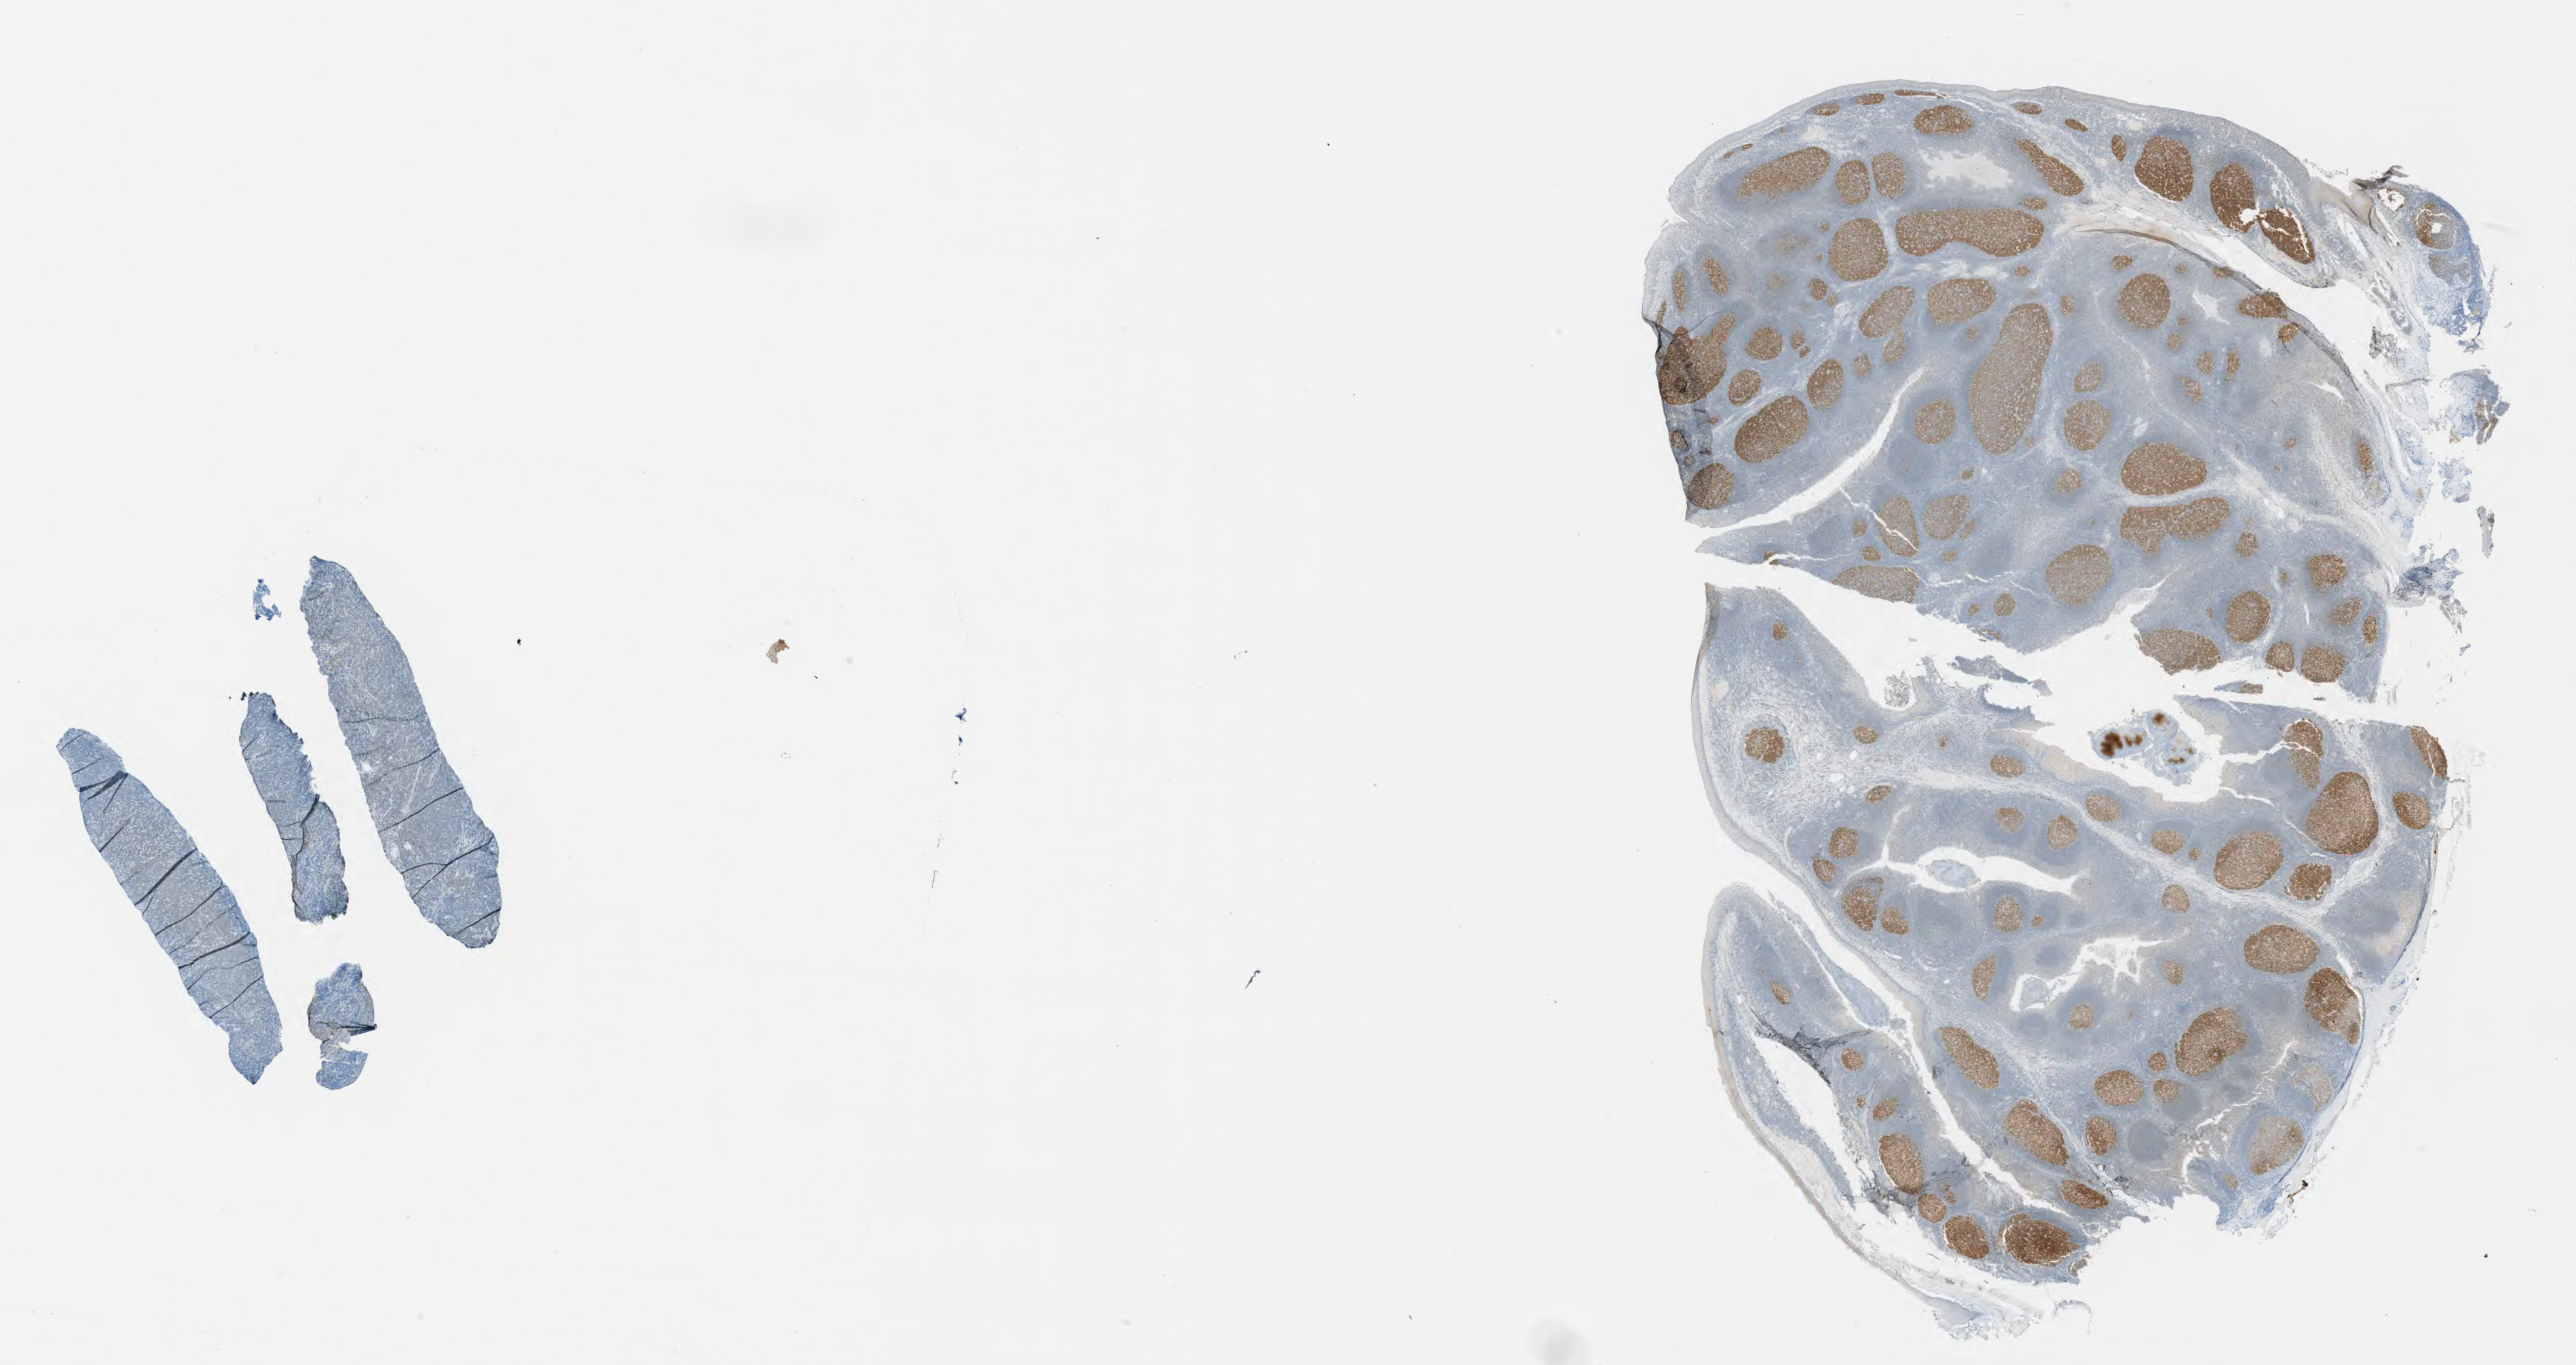
Immunohistochemistry (IHC) whole-slide image stained for BCL6, shown as a low-resolution overview of the whole scanned area (about 29.2 x 15.5 mm), tumor tissue. Female patient, age 46 years.
• histologic diagnosis: Burkitt lymphoma, NOS